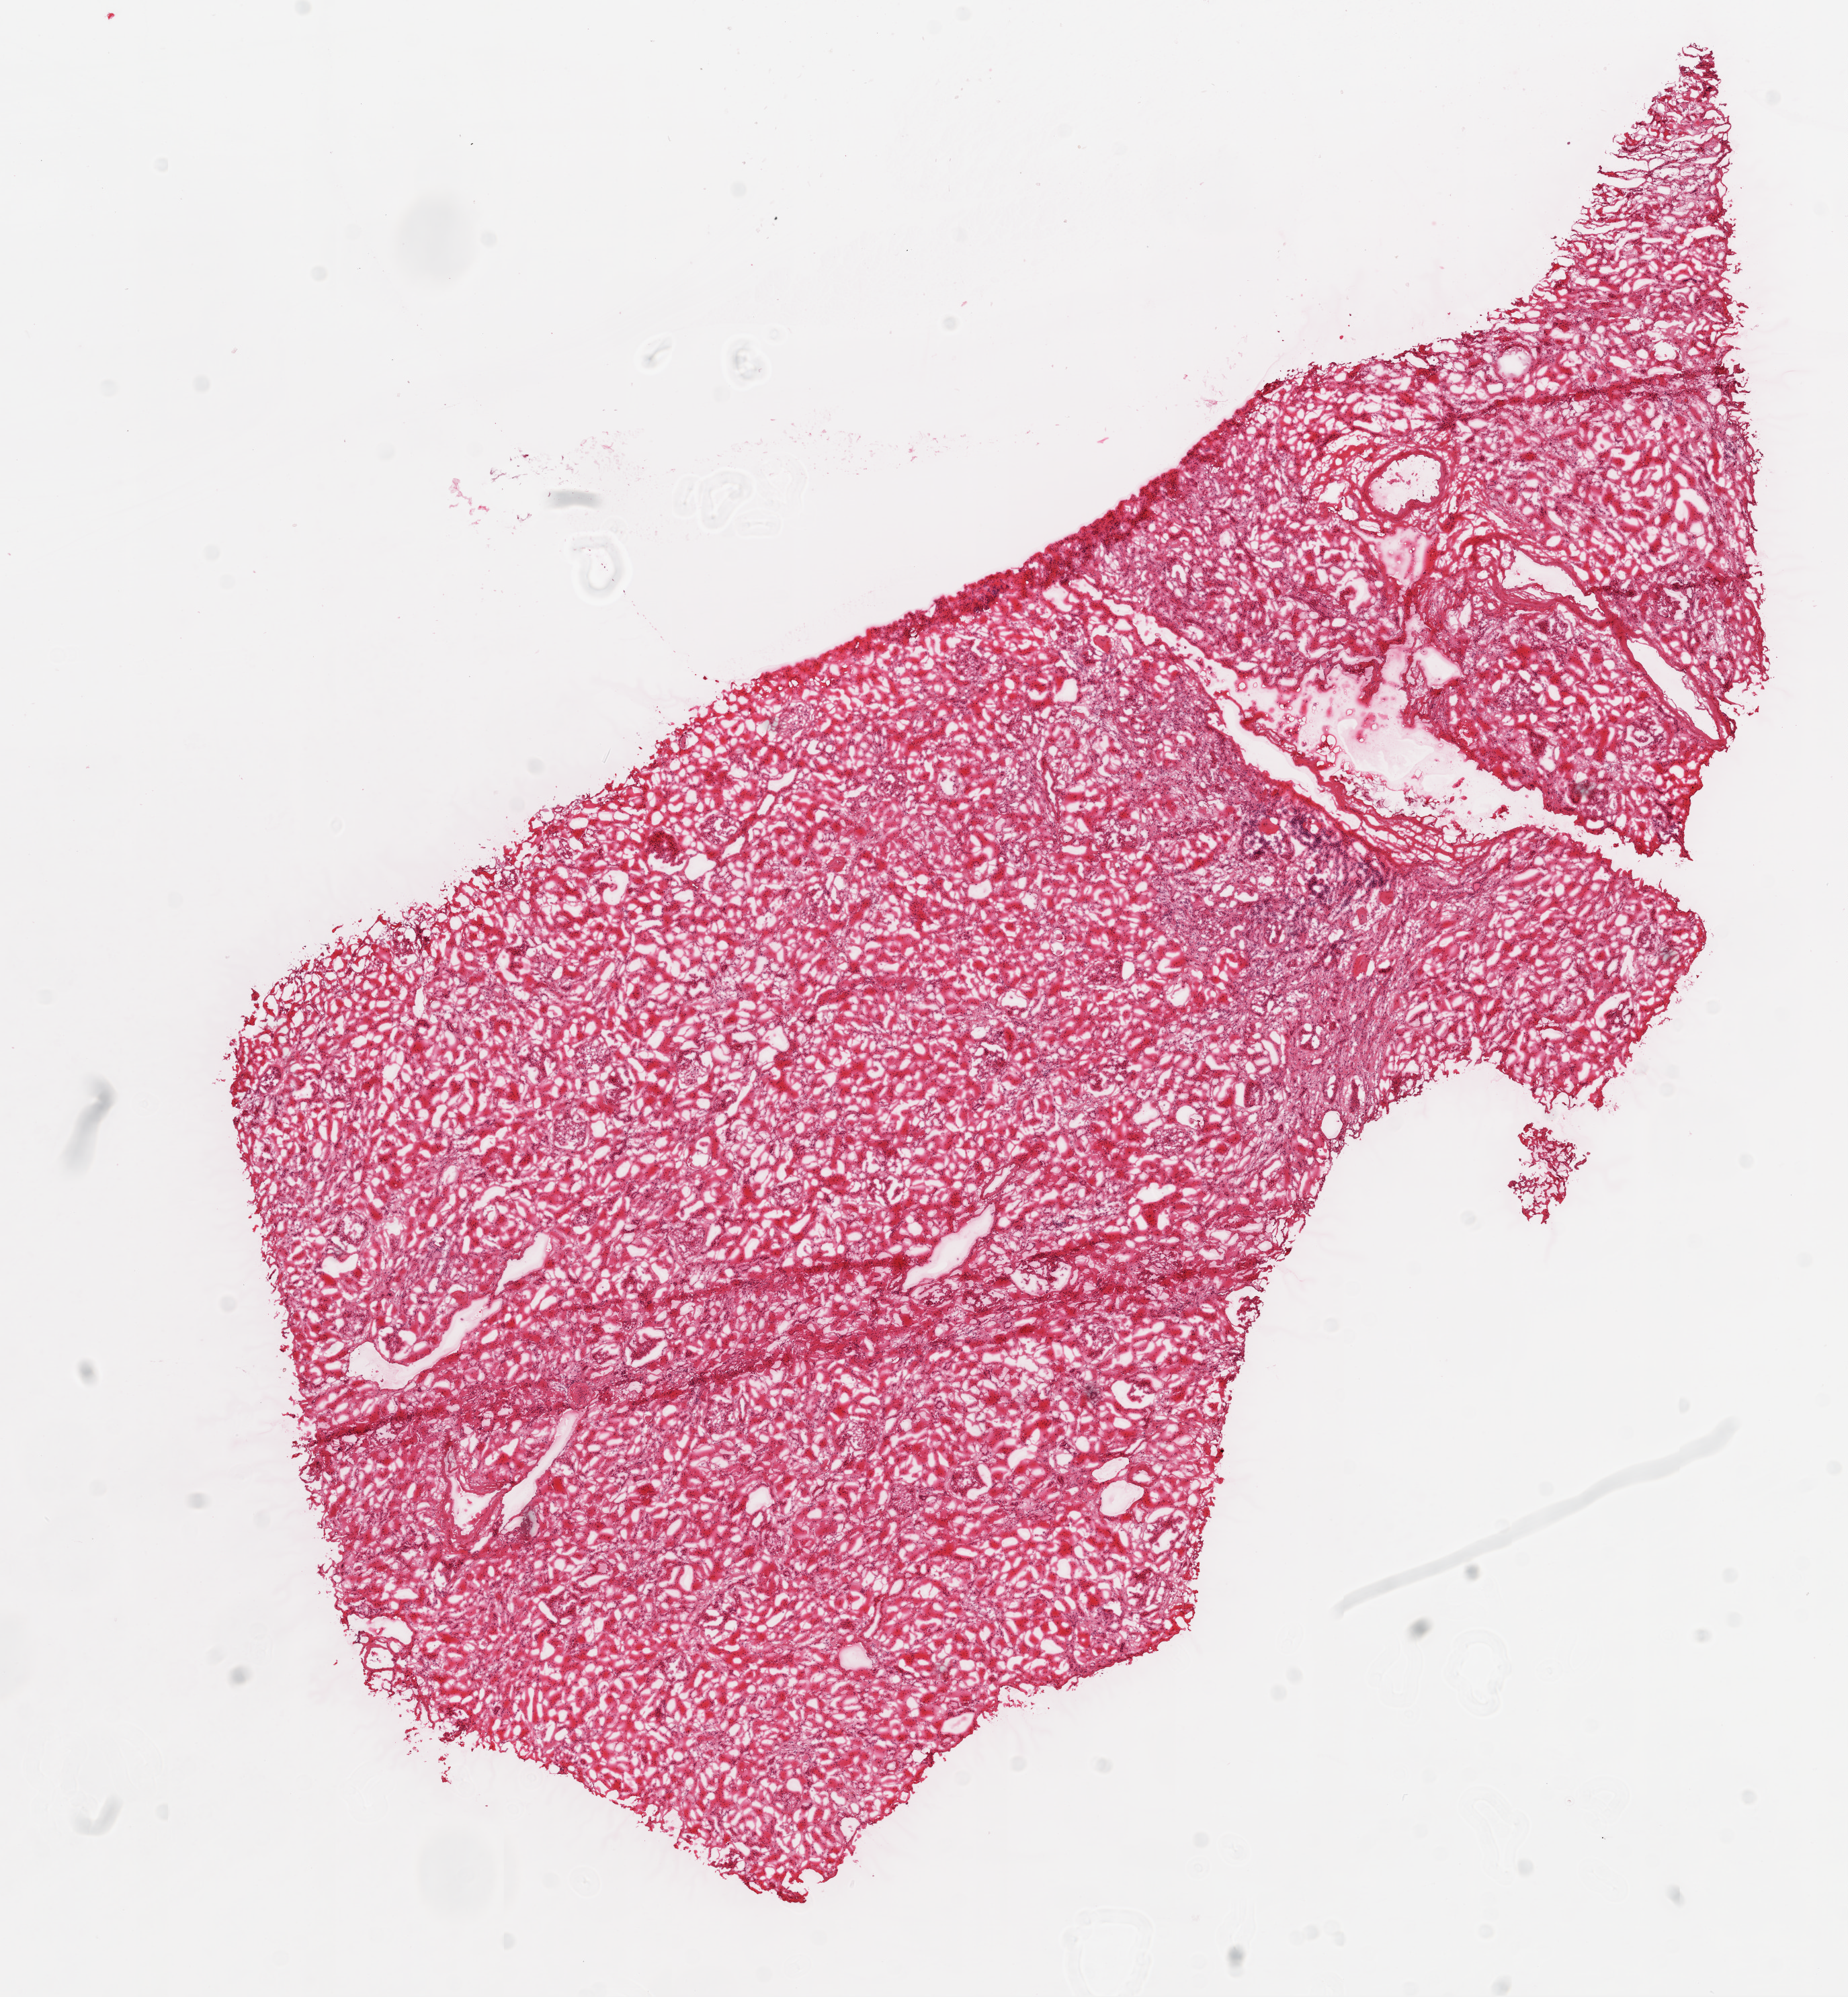
Digitized H&E tissue section (whole slide), low-resolution overview of the scanned area, about 11.0 x 11.9 mm (acquisition: 20x scan), frozen section from the top of the tissue portion, solid tissue normal (non-tumour tissue) sample from the kidney. Patient: female, age at initial diagnosis 64 years.
- this section: solid tissue normal sample (biorepository sample class)
- patient diagnosis: Clear cell adenocarcinoma, NOS